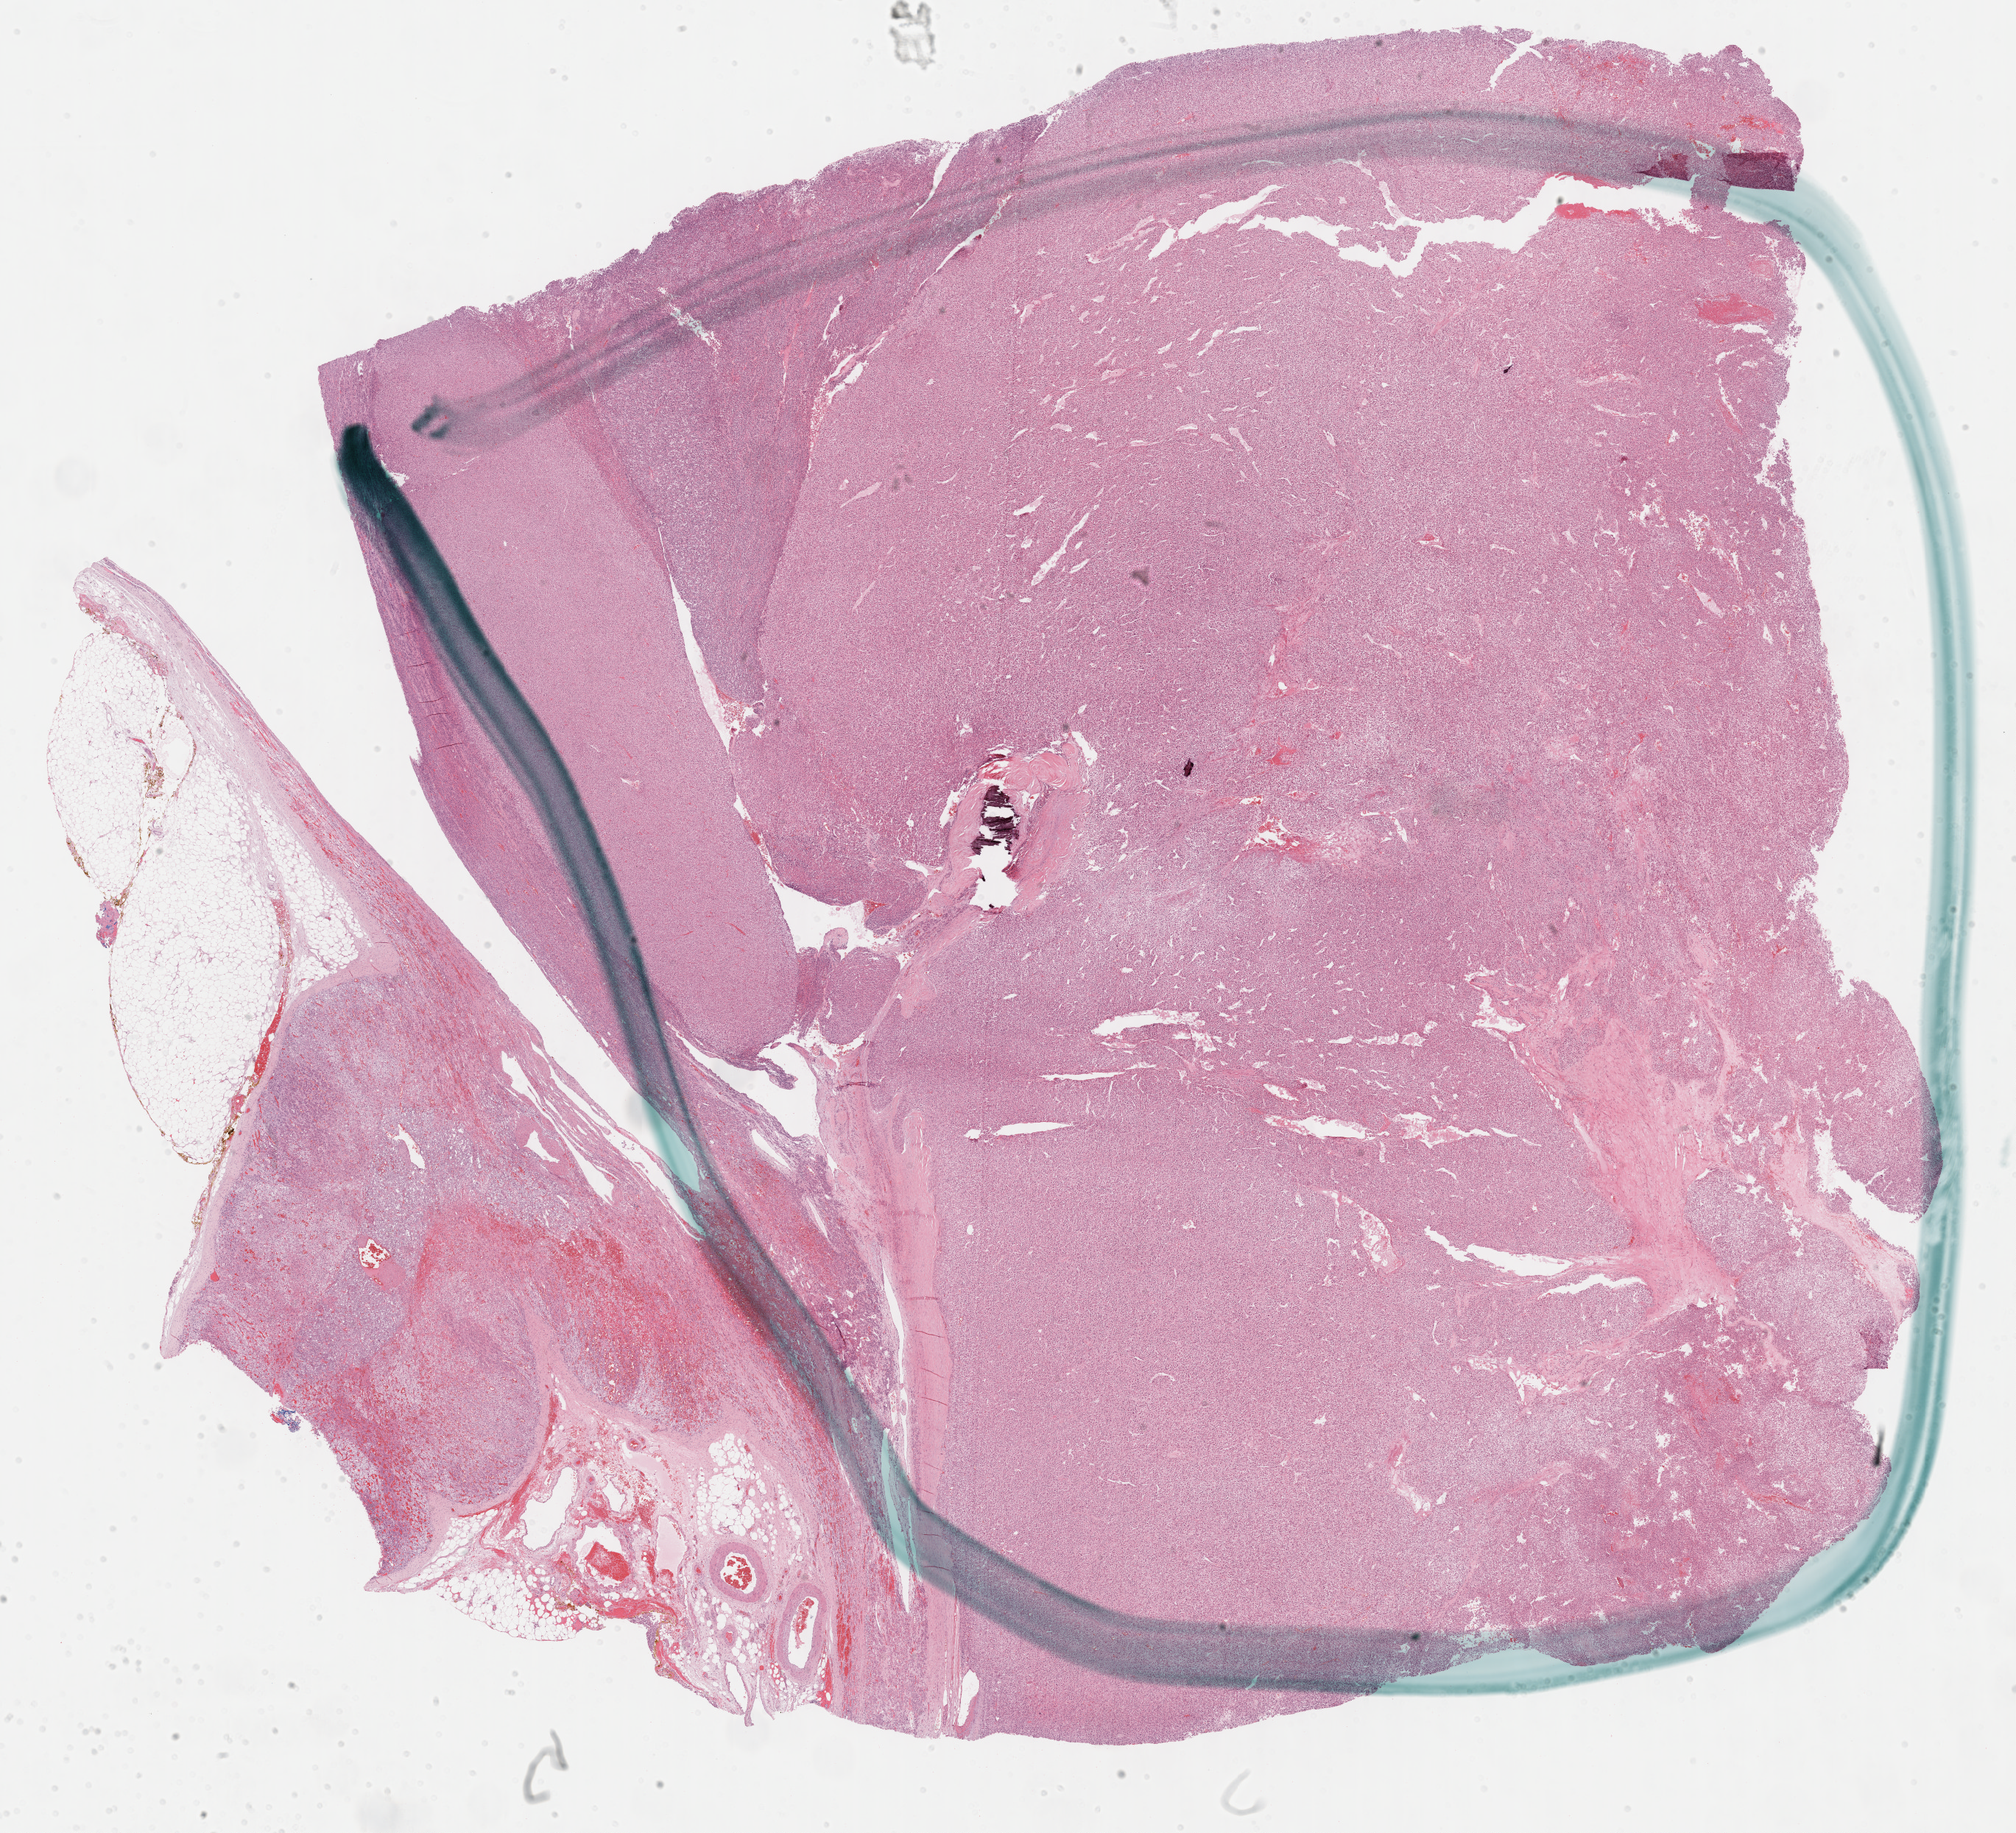
Hematoxylin and eosin (H&E) stained whole-slide image — a low-resolution overview of the entire scanned area, about 22.1 x 20.1 mm (from a 40x scan), formalin-fixed paraffin-embedded (FFPE) diagnostic section, adrenal cortex, primary tumour sample. Male patient; age at initial diagnosis 60 years.
* diagnosis: Adrenal cortical carcinoma
* laterality: left